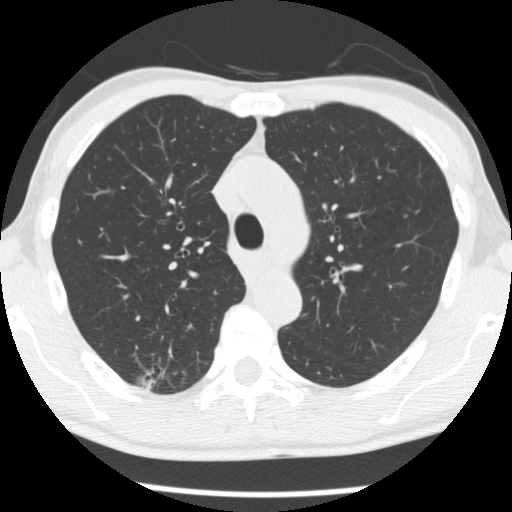
Axial slice from a low-dose chest CT screening exam; baseline annual screen; lung window (W 1500 / L -600 HU); 2.5 mm slice thickness; standard (soft-tissue) reconstruction kernel (STANDARD). Male, age 66 years at enrolment. Former smoker at enrolment.
Expert reader's lesion annotation, box from (x=132, y=356) to (x=189, y=400) px. The screening reader recorded 4 non-calcified nodules or masses ≥4 mm on this exam; which of them this box marks is not recorded. Participant outcome: lung cancer diagnosed 503 days after this screen — adenocarcinoma, NOS, right upper lobe, undifferentiated (G4), stage IA (AJCC 6th edition), 20 mm at pathology.